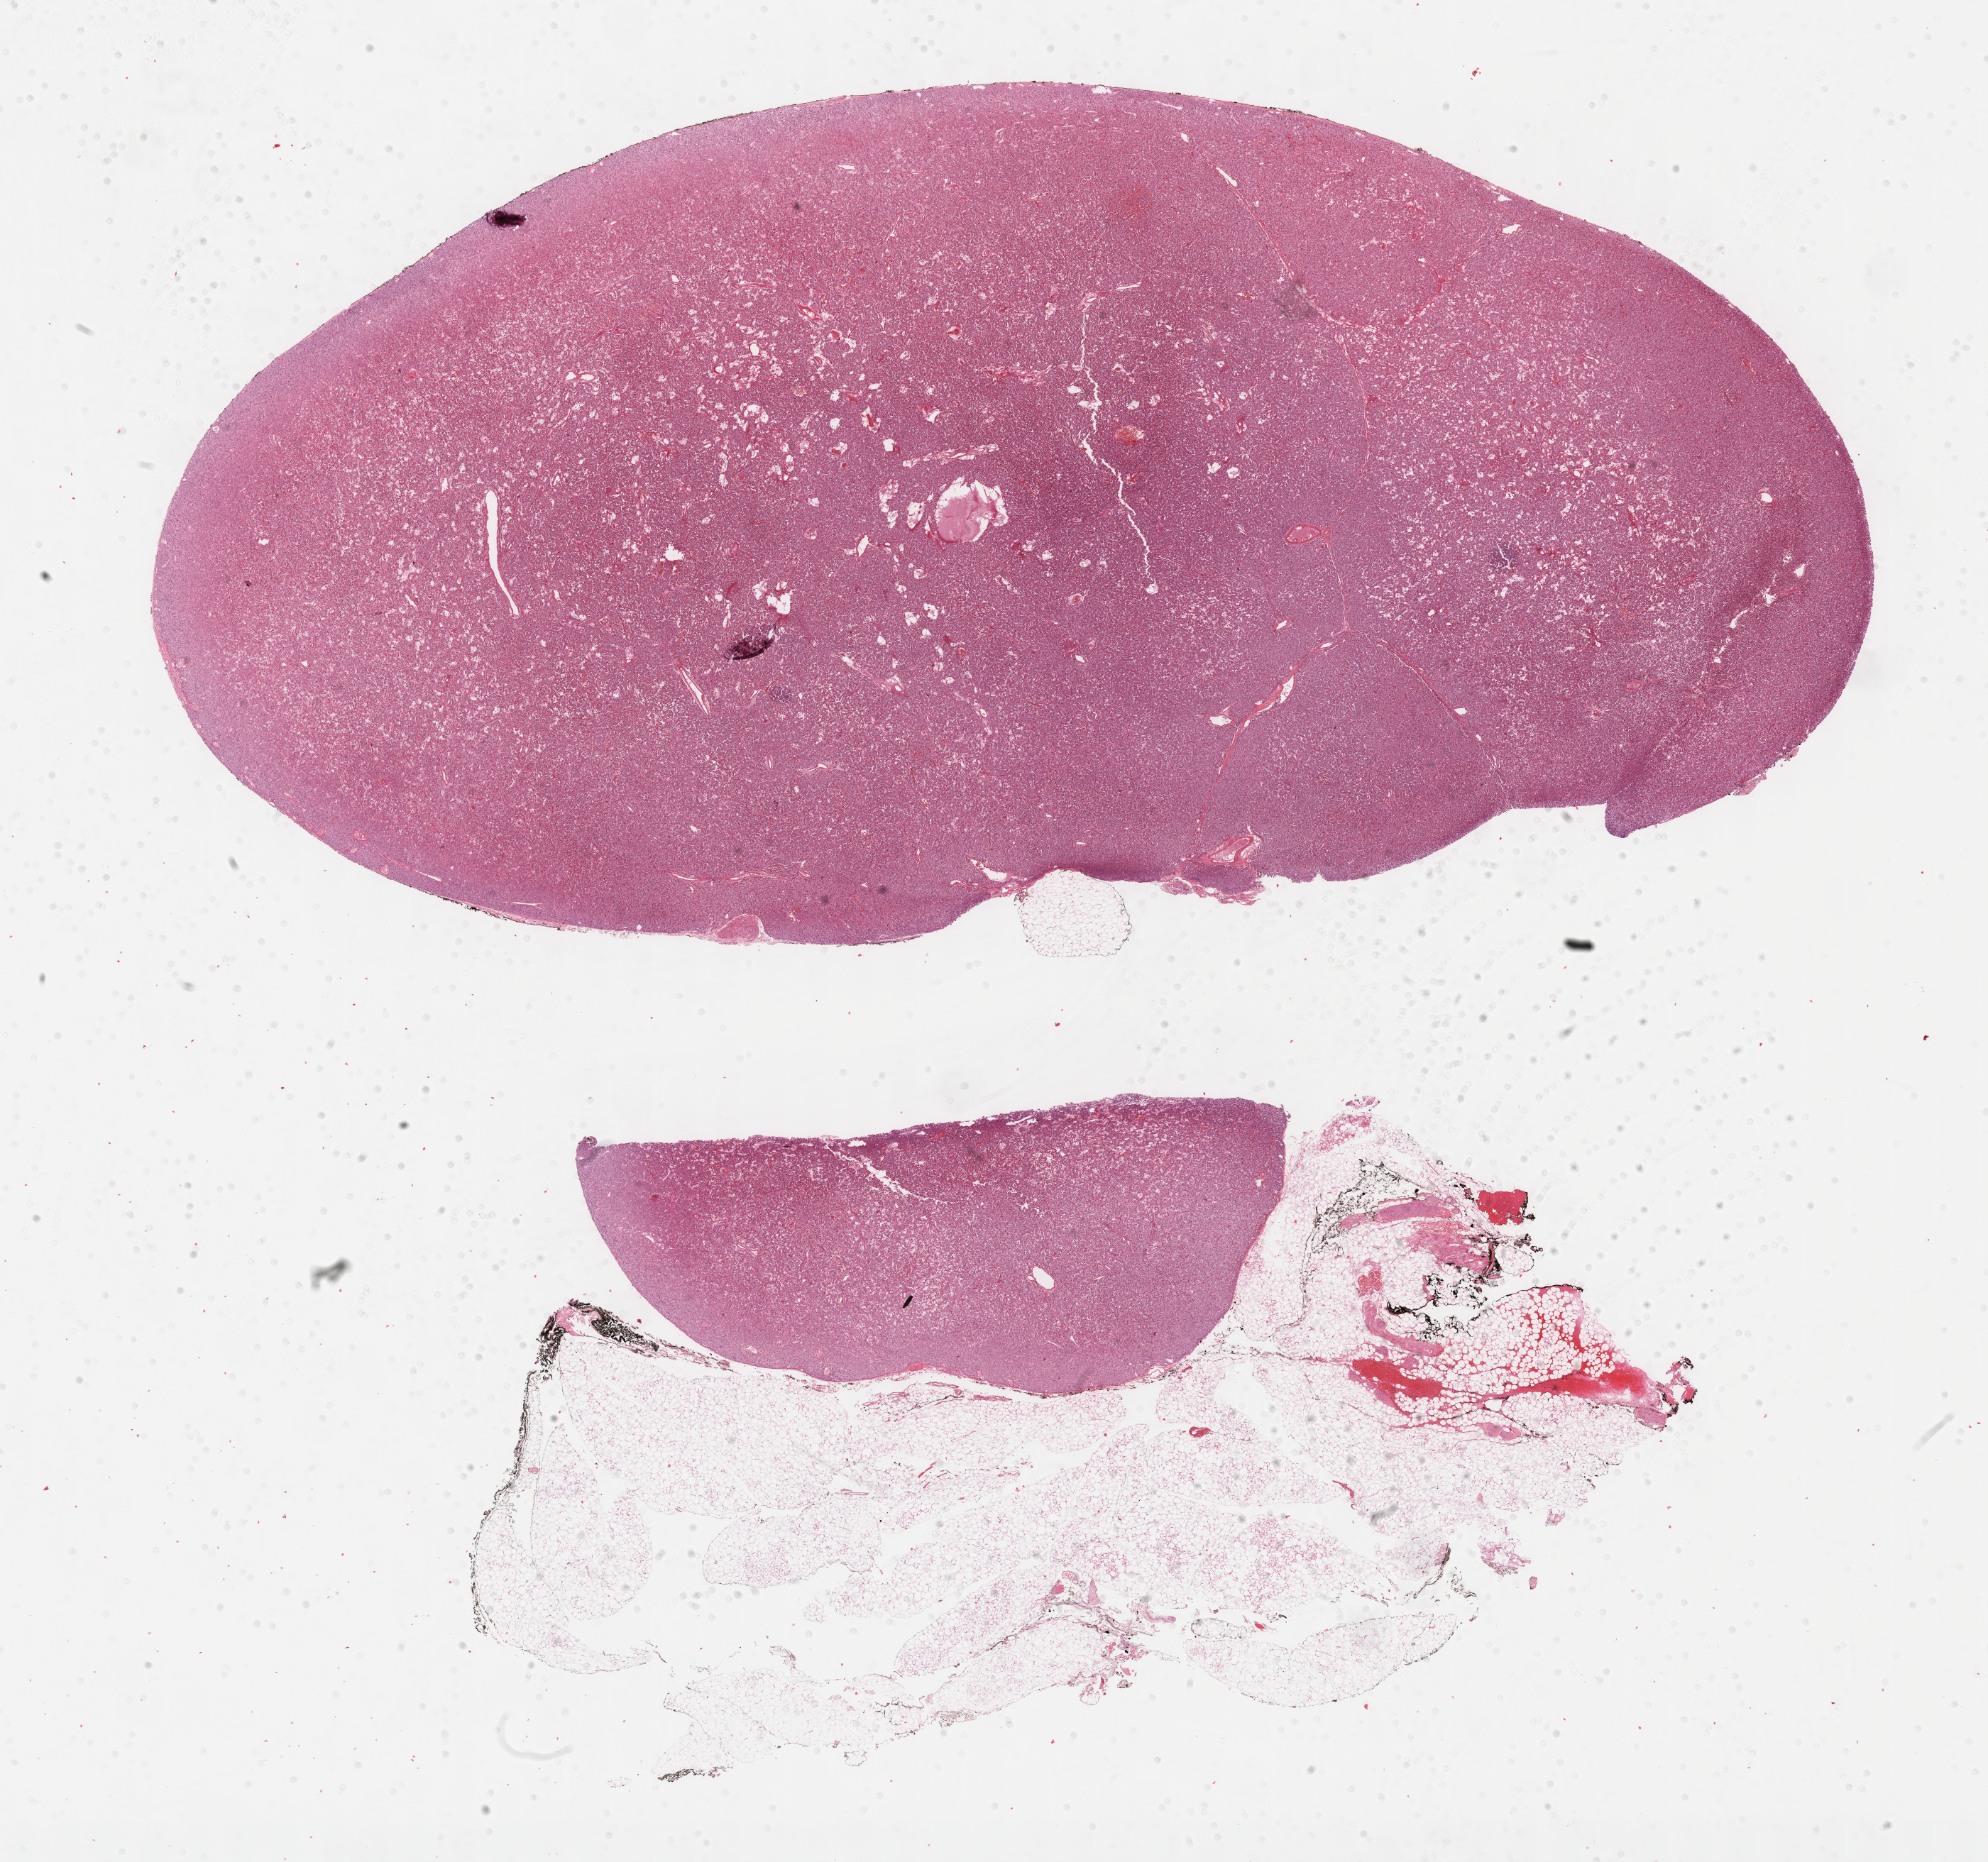
Digitized Hematoxylin and eosin (H&E) stained tissue section (whole slide) — shown as a low-resolution overview of the whole scanned area (about 22.7 x 21.2 mm). Formalin-fixed paraffin-embedded (FFPE) diagnostic section. Sample: primary tumour, retroperitoneum and peritoneum. Female, age 69 years at initial diagnosis.
Diagnosis: Extra-adrenal paraganglioma, NOS (retroperitoneum).